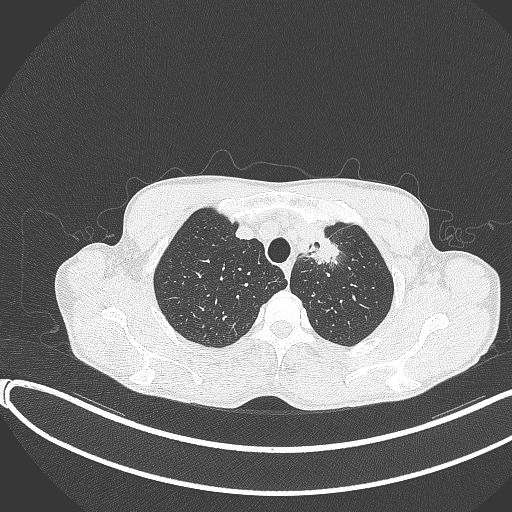
Chest CT, one axial slice; slice 326 of 374 in the series (ordered by position); reconstruction kernel B70f; 120 kVp; lung window (W 1500 / L -600 HU); 512 × 512 image matrix. Patient: male, 58 years. Case-level facts recorded for this patient, not image findings: clinical TNM (as recorded): T1c N1 M0.
Structures marked on this image (bounding box drawn by a radiologist):
- lung tumour (recorded histology: adenocarcinoma): box from (x=302, y=227) to (x=341, y=268) px